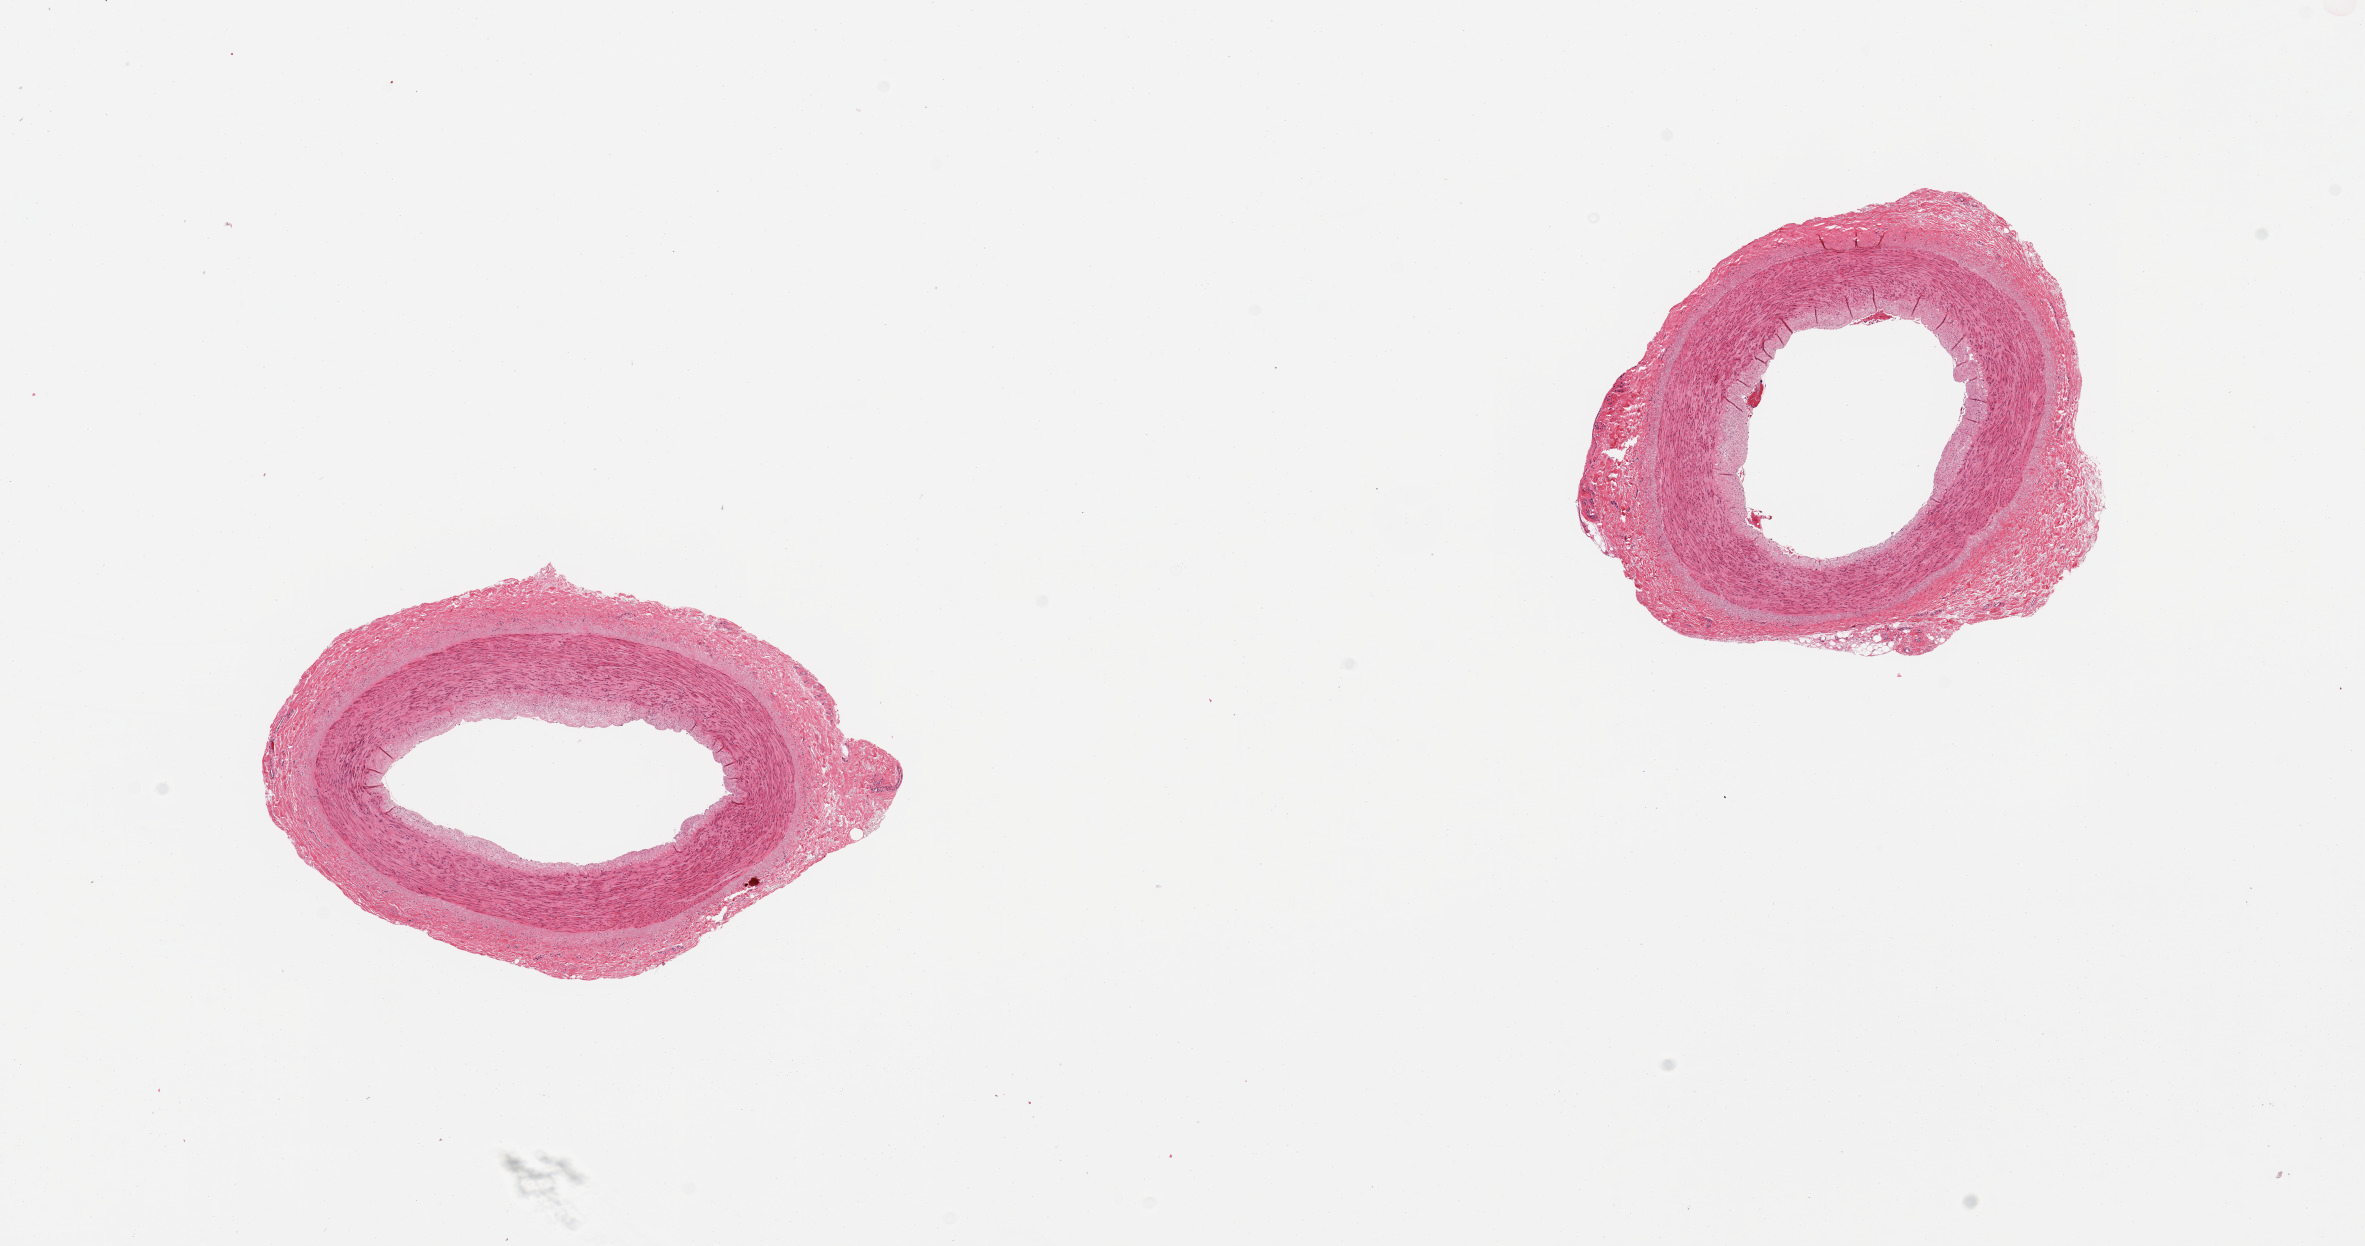
Whole-slide image, haematoxylin and eosin stain, shown as a low-resolution overview of the whole scanned area (about 18.7 x 9.9 mm, slide scanned at 20x), PAXgene-fixed, paraffin-embedded tissue, target tissue: tibial artery, tissue donor sample. Male donor.
Reviewer comment on this tissue sample: 2 pieces; well trimmed; no lesions.